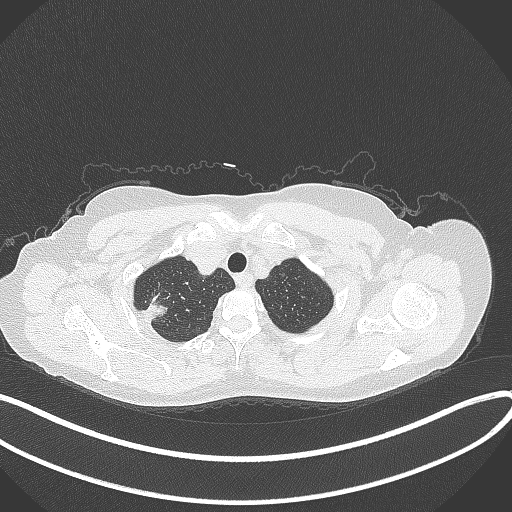
Chest CT, one axial slice. Position 324 of 337 along the scan axis. Reconstruction kernel B70f. 120 kVp. Lung window (W 1500 / L -600 HU). 1 mm slice thickness. 512 × 512 image matrix, field of view 400 × 400 mm. Patient: female, 50 years. Case-level facts recorded for this patient, not image findings: clinical TNM (as recorded): T1c N0 M0; histopathological grade: G2-3.
Annotated regions visible in this slice (bounding box drawn by a radiologist):
- lung tumour (recorded histology: adenocarcinoma): bounding box <144,300,169,323> (left, top, right, bottom; pixels)